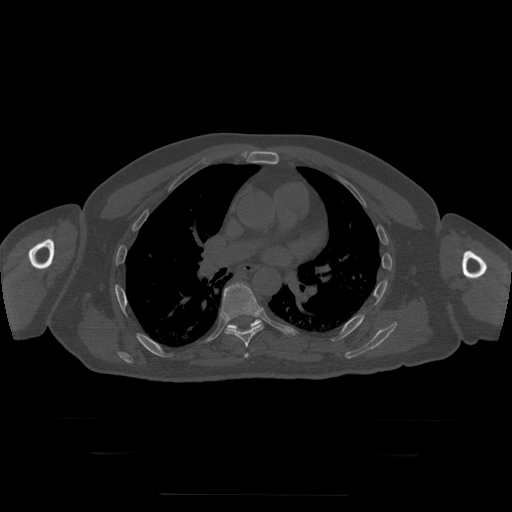
CT including the spine, one axial slice; position 182 of 397 along the scan axis; reconstruction kernel STANDARD; bone window (W 1800 / L 400 HU); 512 × 512 image matrix, field of view 510 × 510 mm. Patient age 73 years. From the clinical record (not read from this slice): primary cancer: prostate.
Structures marked on this image (semi-automatic segmentation, software-assisted and operator-edited):
- T6 vertebra: bounding box (x1, y1, x2, y2) in pixels: (244, 354, 249, 358)
- T7 vertebra: (221, 283, 264, 348)
- T8 vertebra: (228, 320, 262, 331)